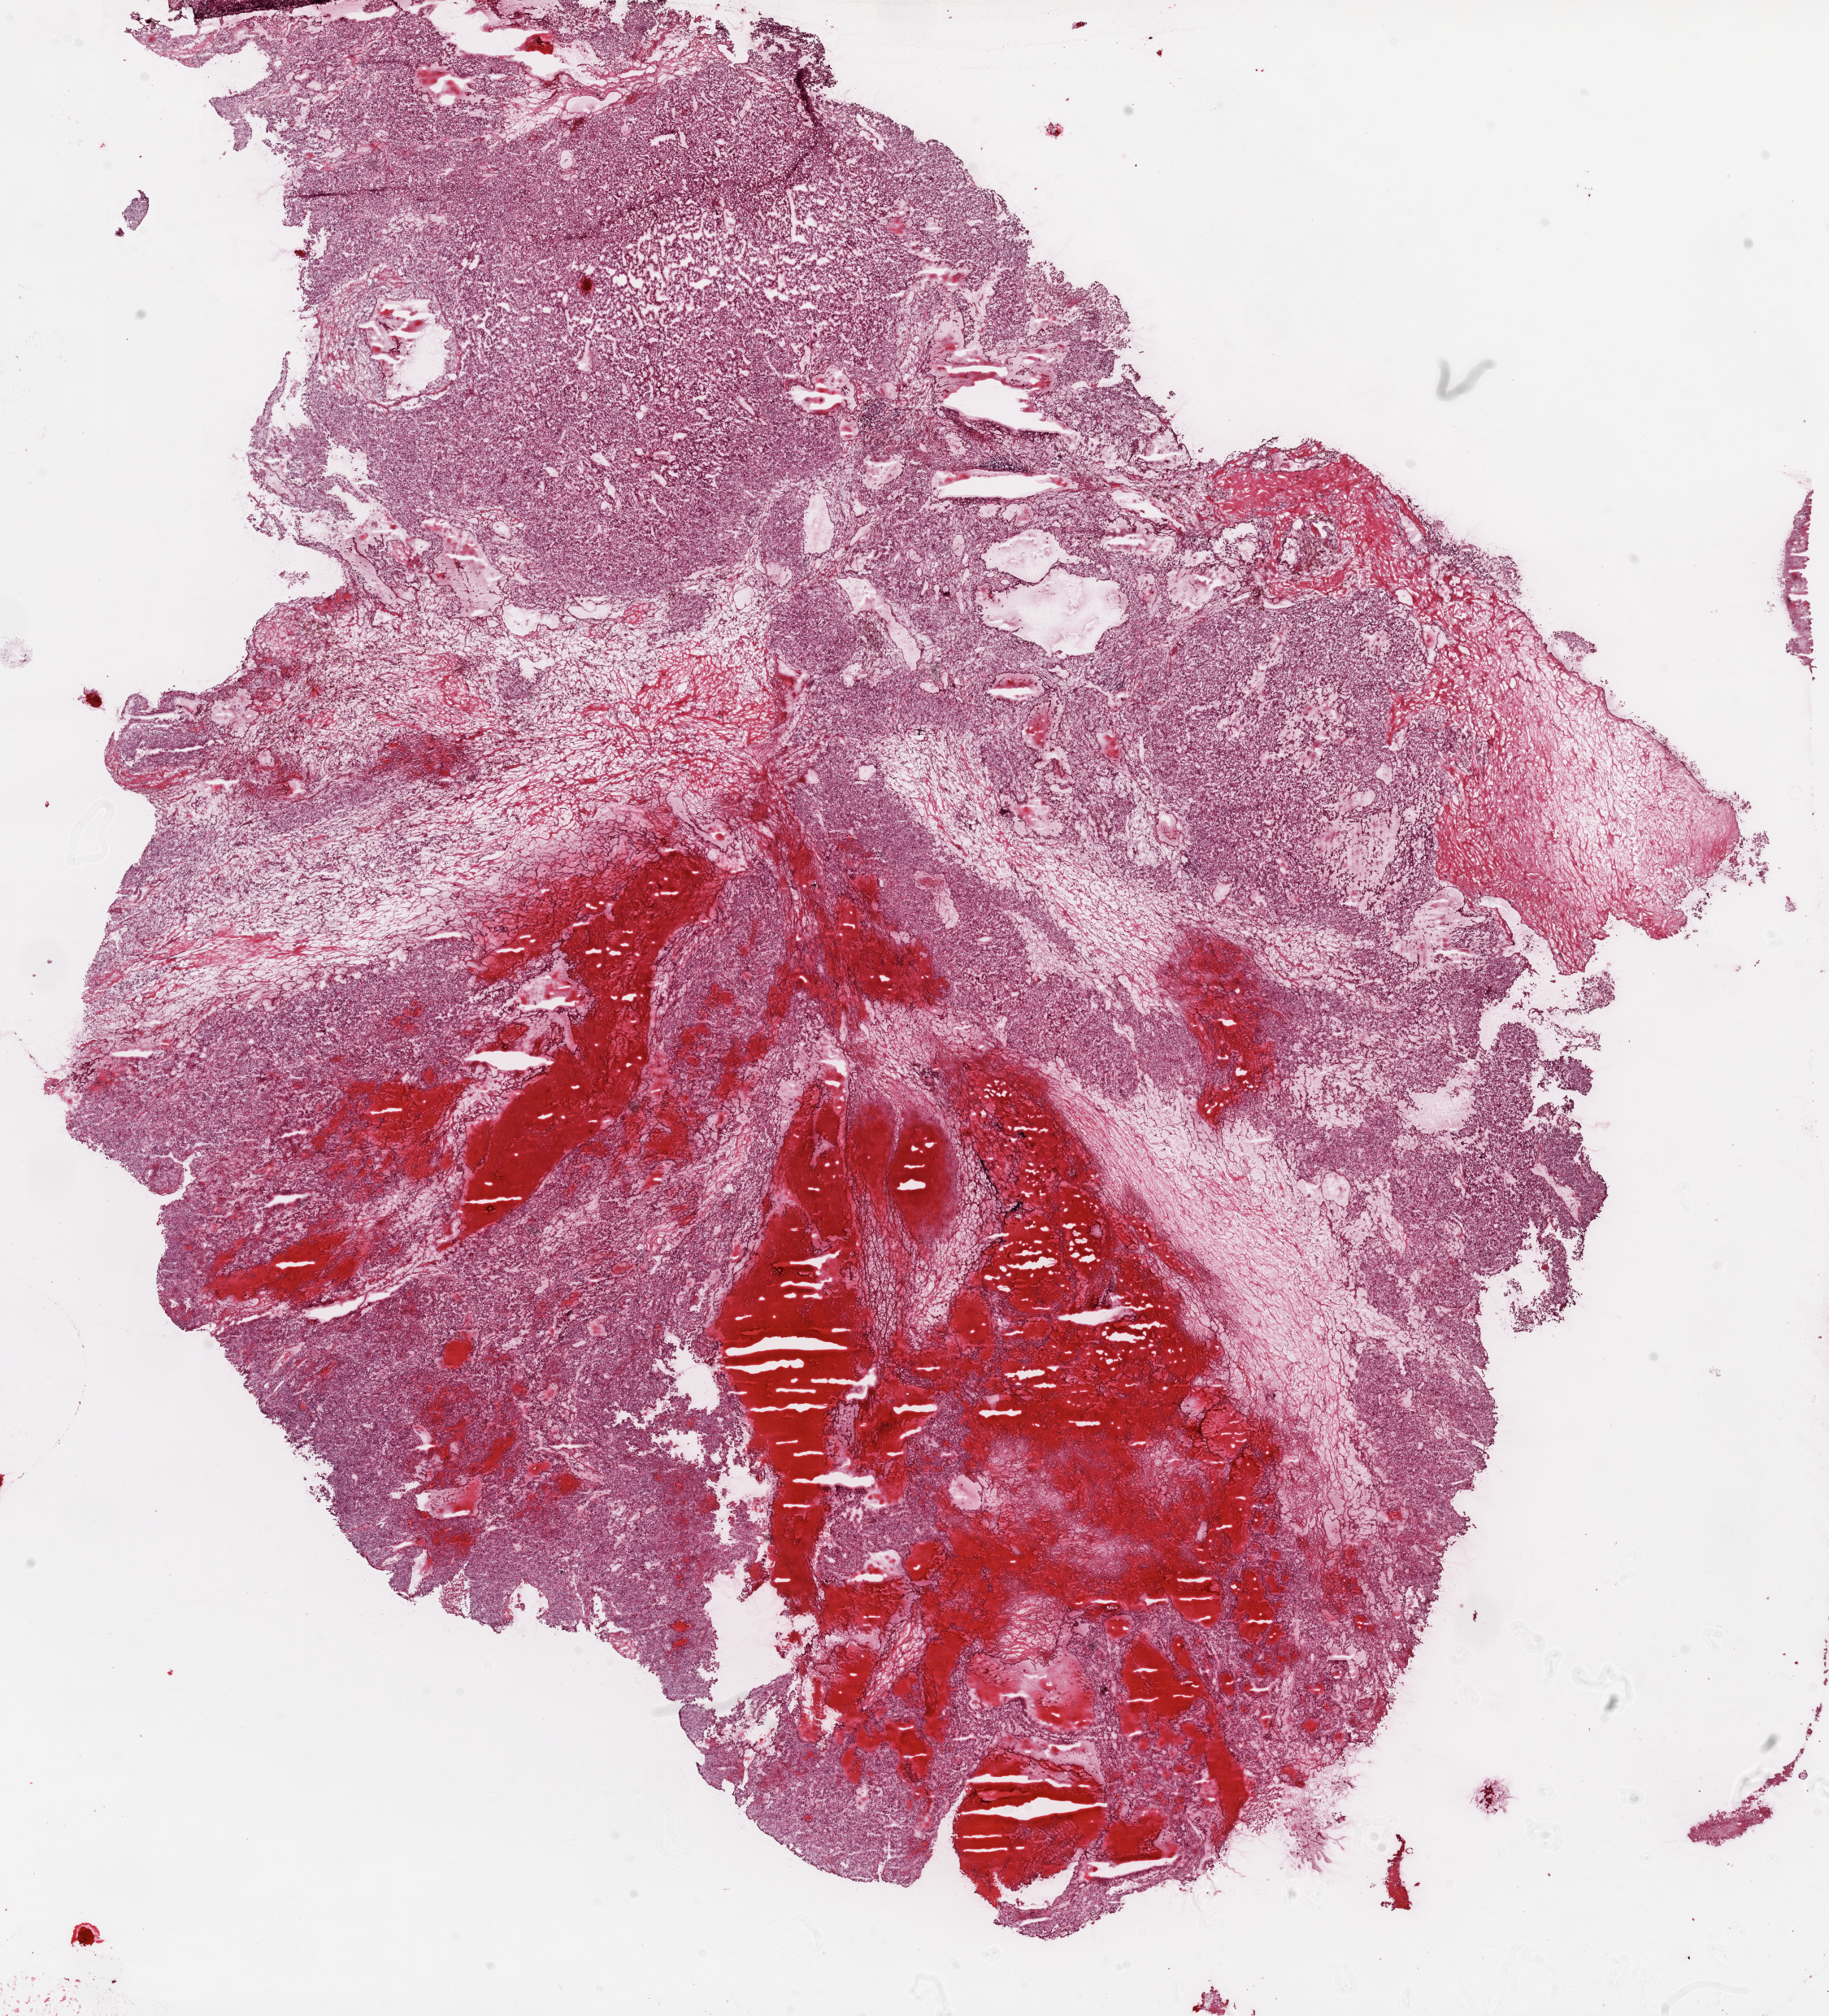
Hematoxylin and eosin (H&E) stained whole-slide image, a low-resolution overview of the entire scanned area, about 18.1 x 19.9 mm (slide scanned at 20x). Frozen section. Kidney, primary tumour sample. Male, age 44 years at initial diagnosis. Histologic grade: G4 (undifferentiated). Pathologist review of this section (percent, as recorded): tumour cells 65%, tumour nuclei 80%, normal cells 0%, stromal cells 35%, necrosis 0%.
Laterality: right. Pathologic diagnosis: Clear cell adenocarcinoma, NOS. AJCC pathologic stage: II.